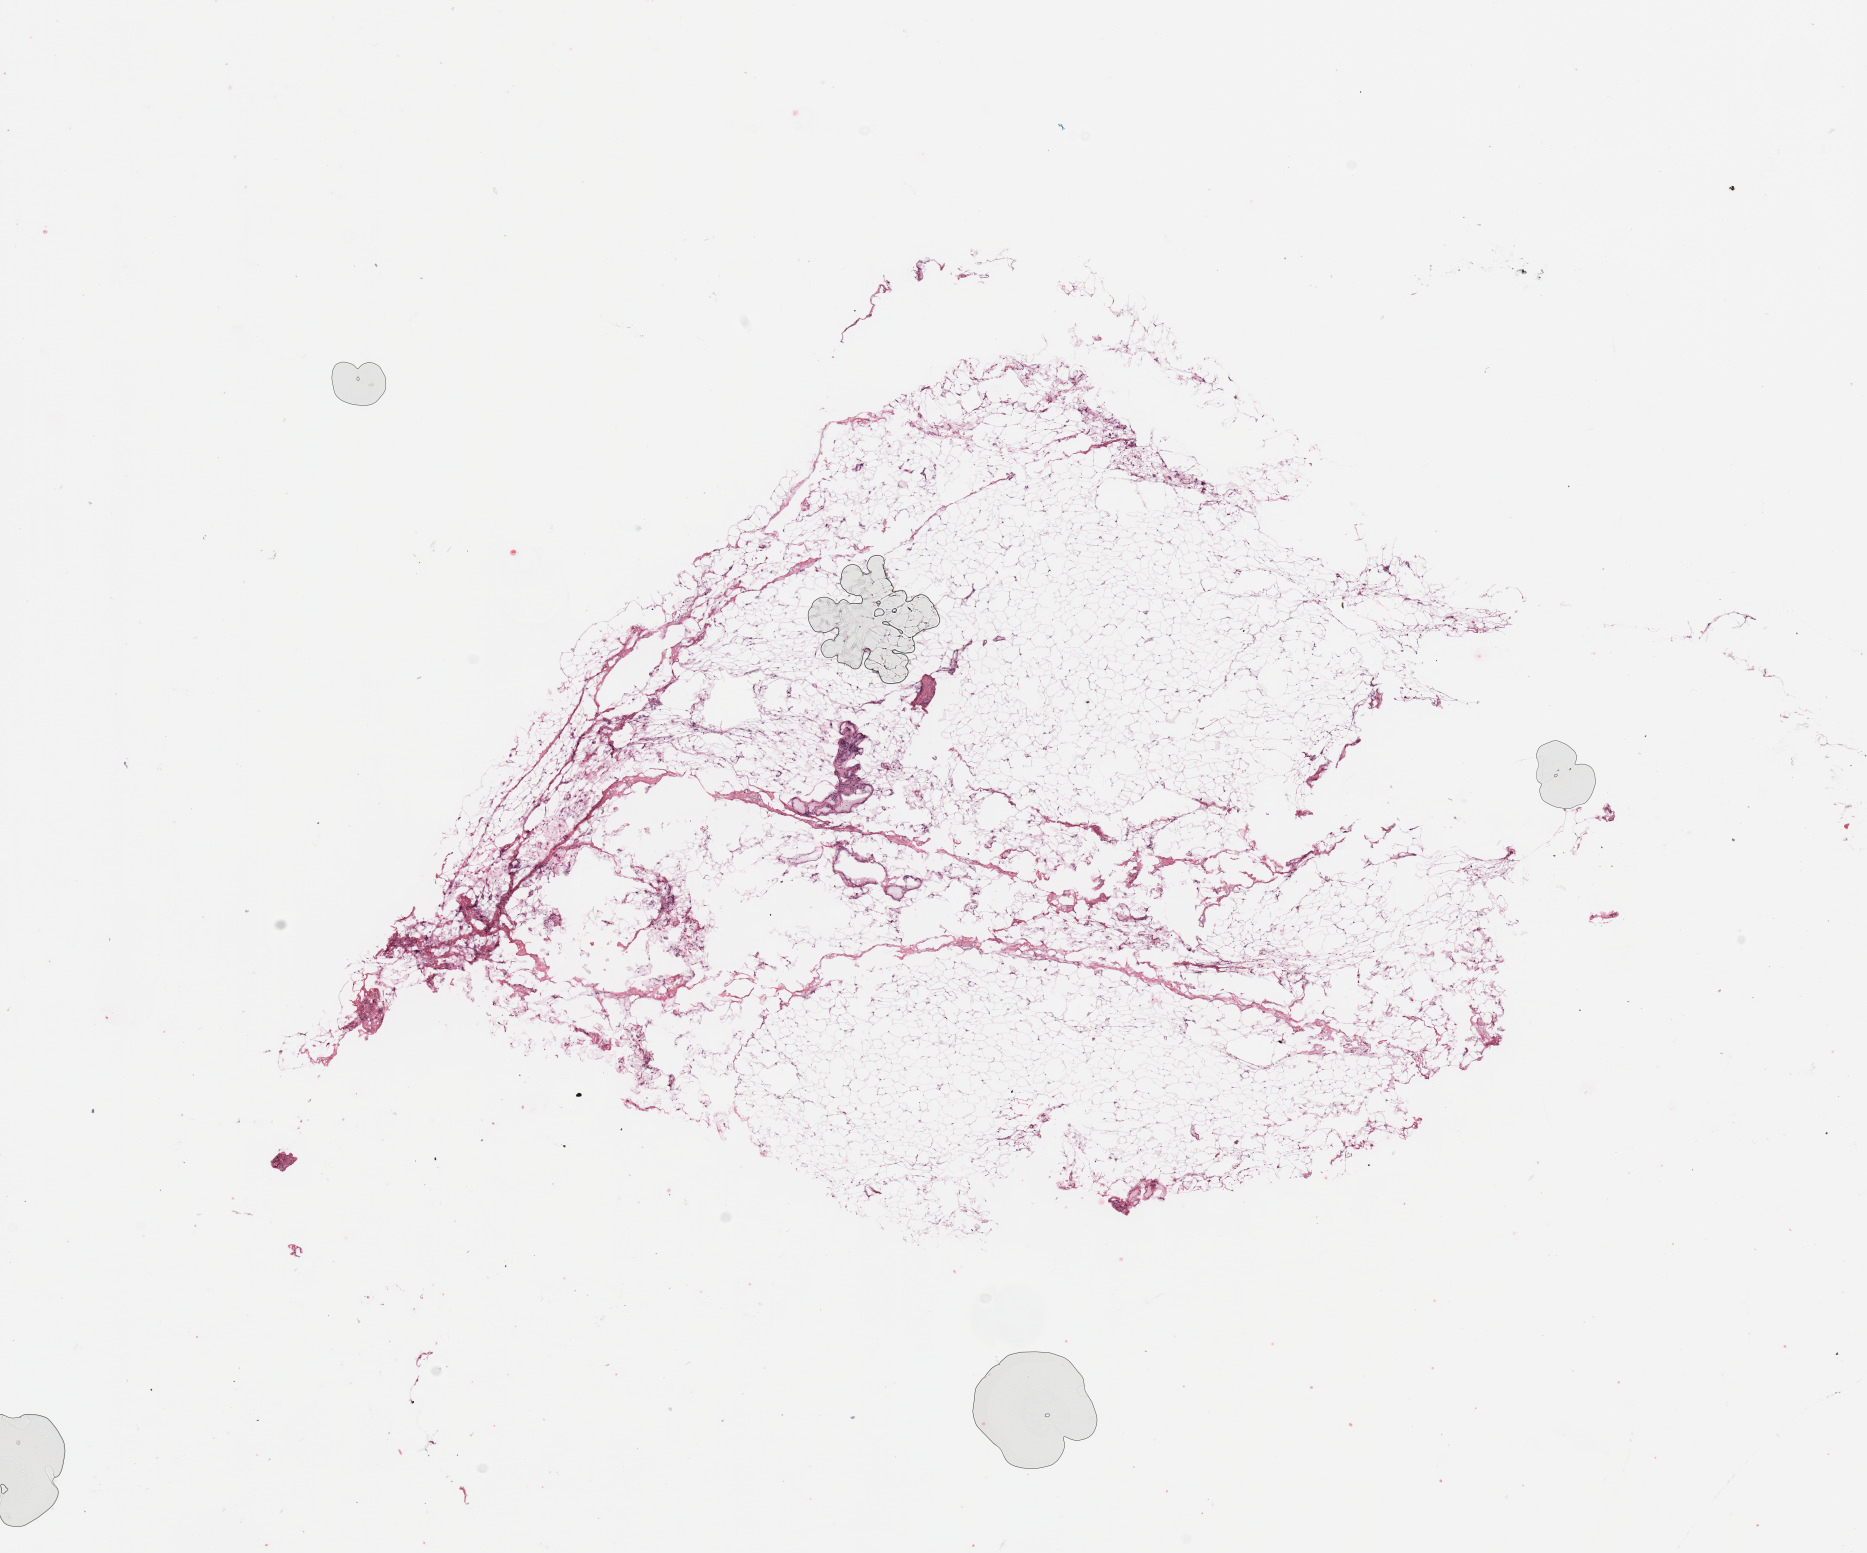
Whole-slide histology image, H&E-stained — shown as a low-resolution overview of the whole scanned area (about 14.8 x 12.3 mm, acquisition: 20x scan). Tumour tissue sample, breast. 66-year-old female patient.
- AJCC pathologic stage: IIIA
- diagnosis: Infiltrating duct carcinoma, NOS